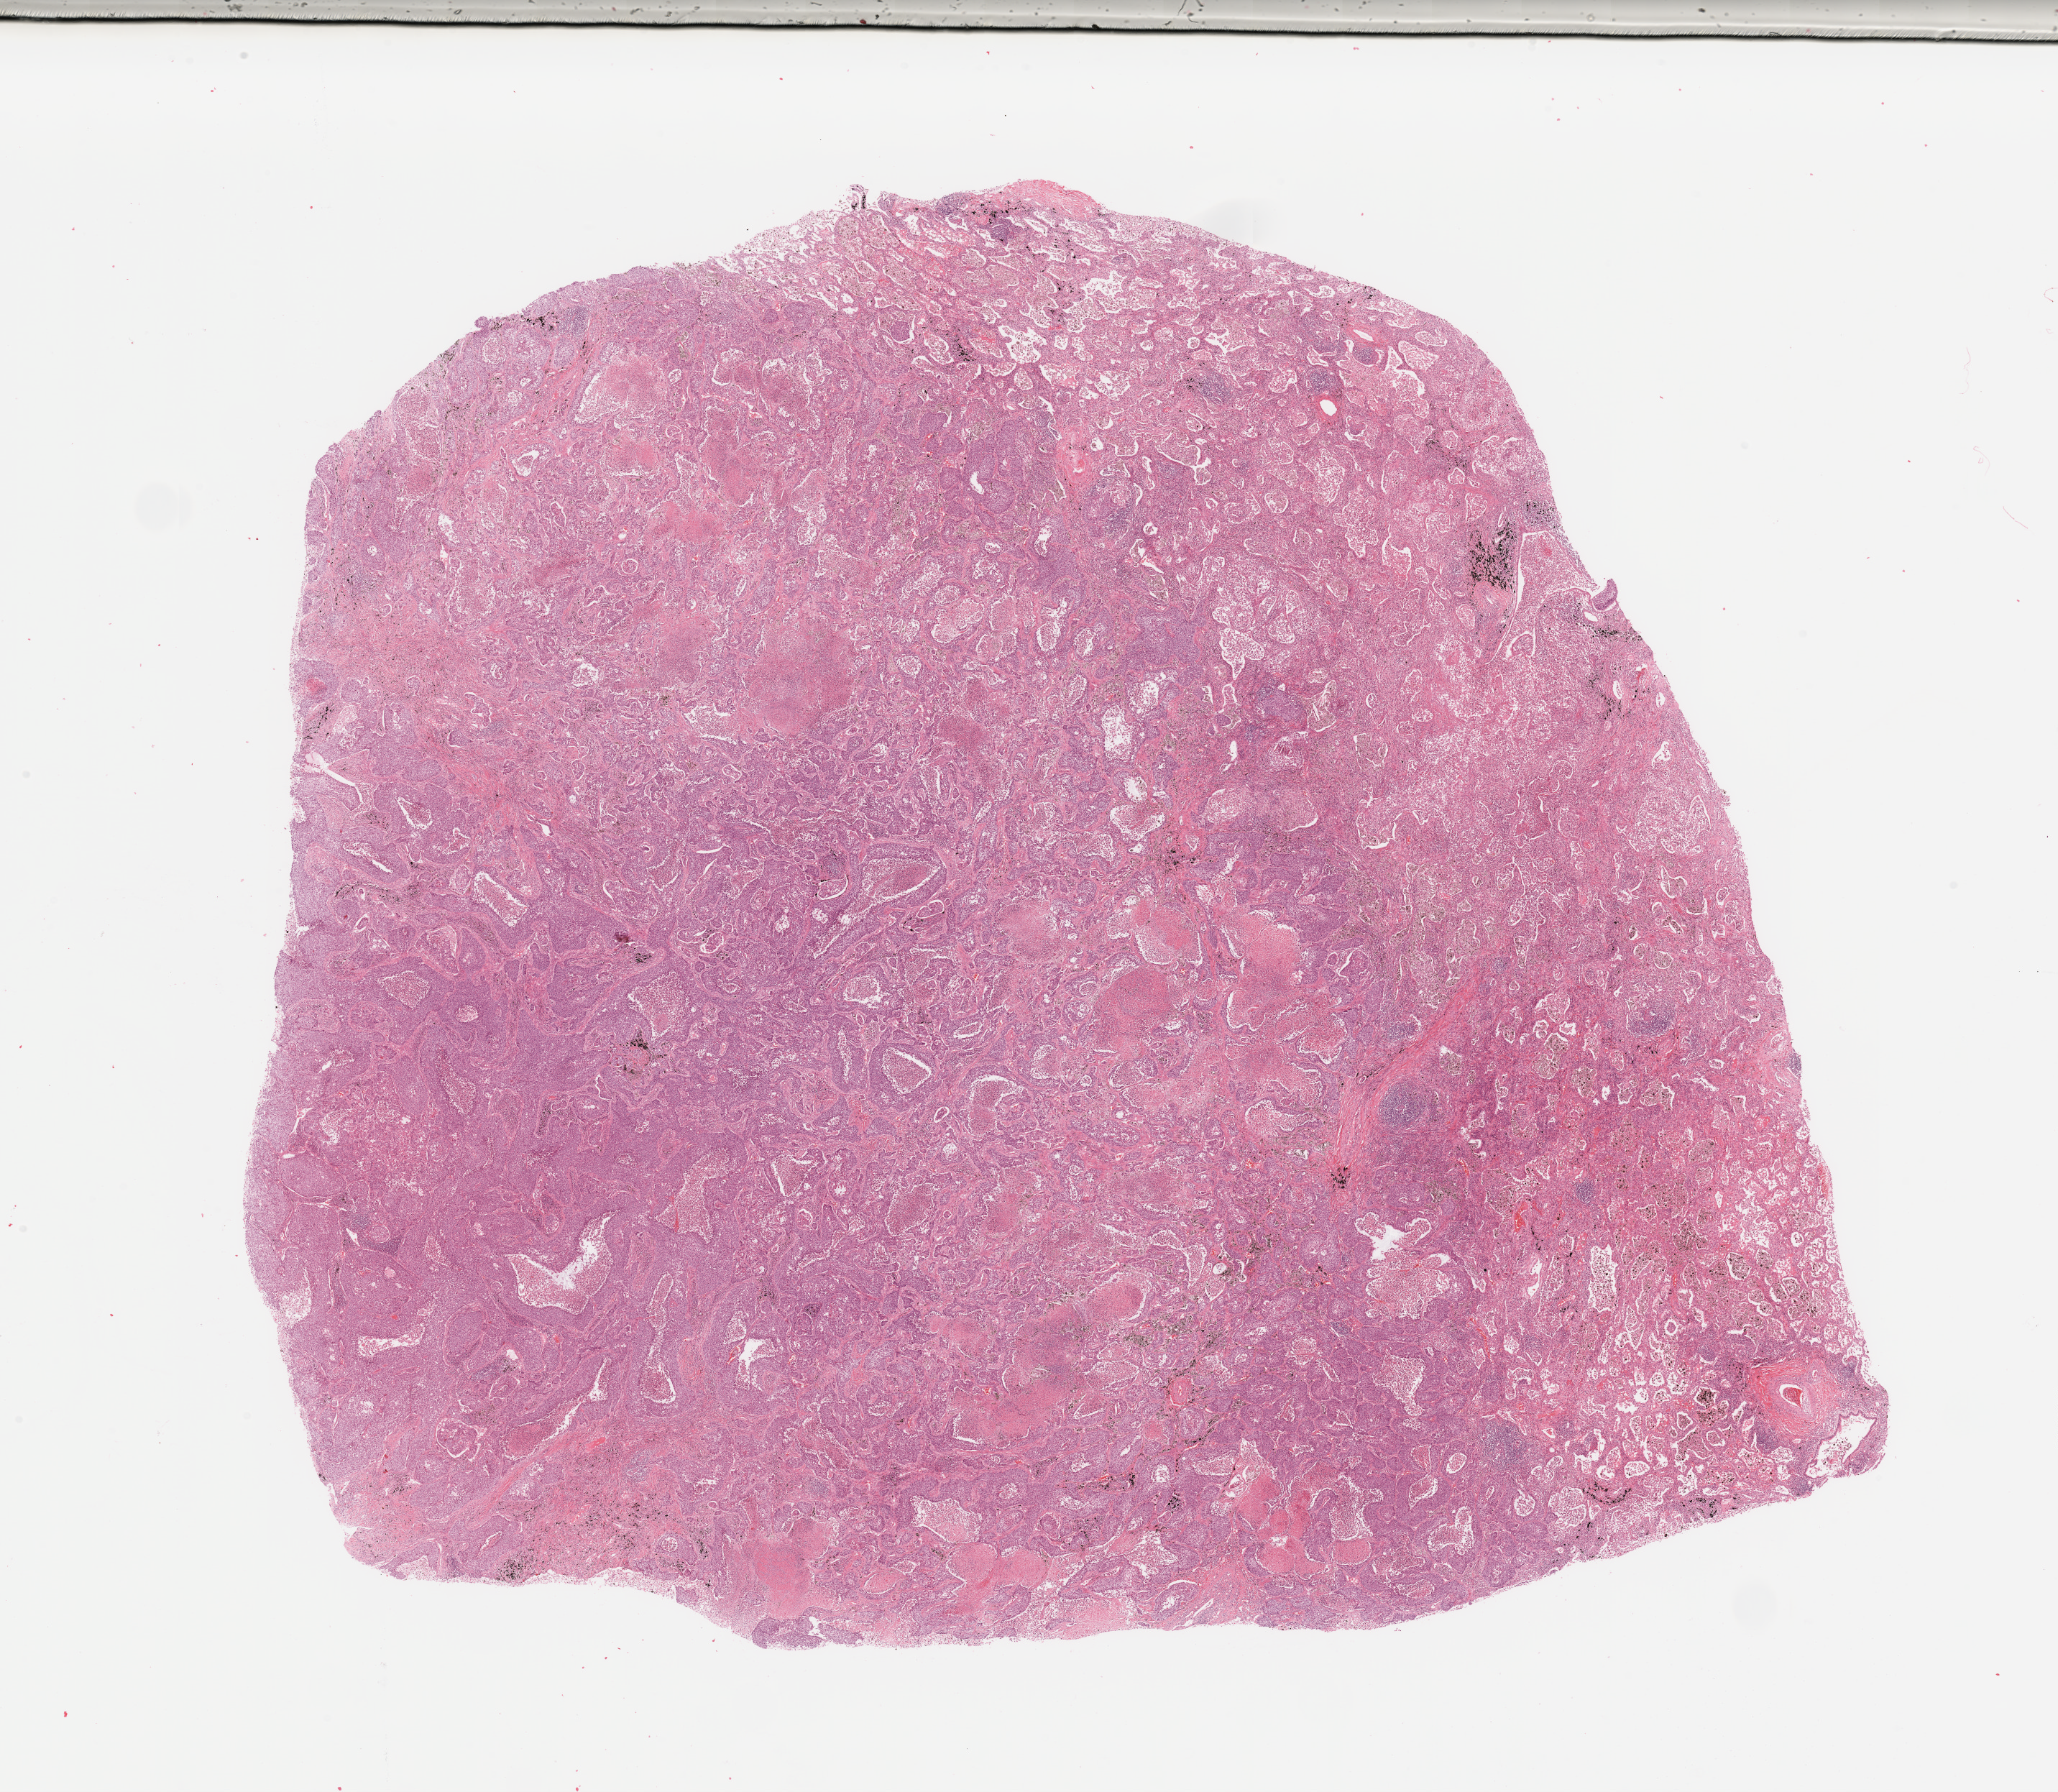
Digitized H&E-stained tissue section (whole slide), low-resolution overview of the scanned area, about 22.6 x 19.7 mm; lung, tumour tissue. 52-year-old male patient. Histologic grade: G3 (poorly differentiated).
* histologic diagnosis: Squamous cell carcinoma, NOS
* AJCC pathologic stage: IIB